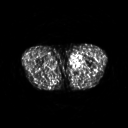
FDG PET of an extremity soft-tissue mass (from a PET/CT study), one axial slice. Slice 246 of 311 in the series (ordered by position). 3.27 mm slice thickness. 128 × 128 image matrix. Patient: male, 29 years. From the clinical record (not read from this slice): histological type: mixoid liposarcoma; grade: low; site of the primary tumour: left thigh.
Outlined on this slice (expert contour drawn on MRI and transferred to this co-registered scan by the dataset authors):
- gross tumour volume (mass): bounding box <70,53,83,69> (left, top, right, bottom; pixels)